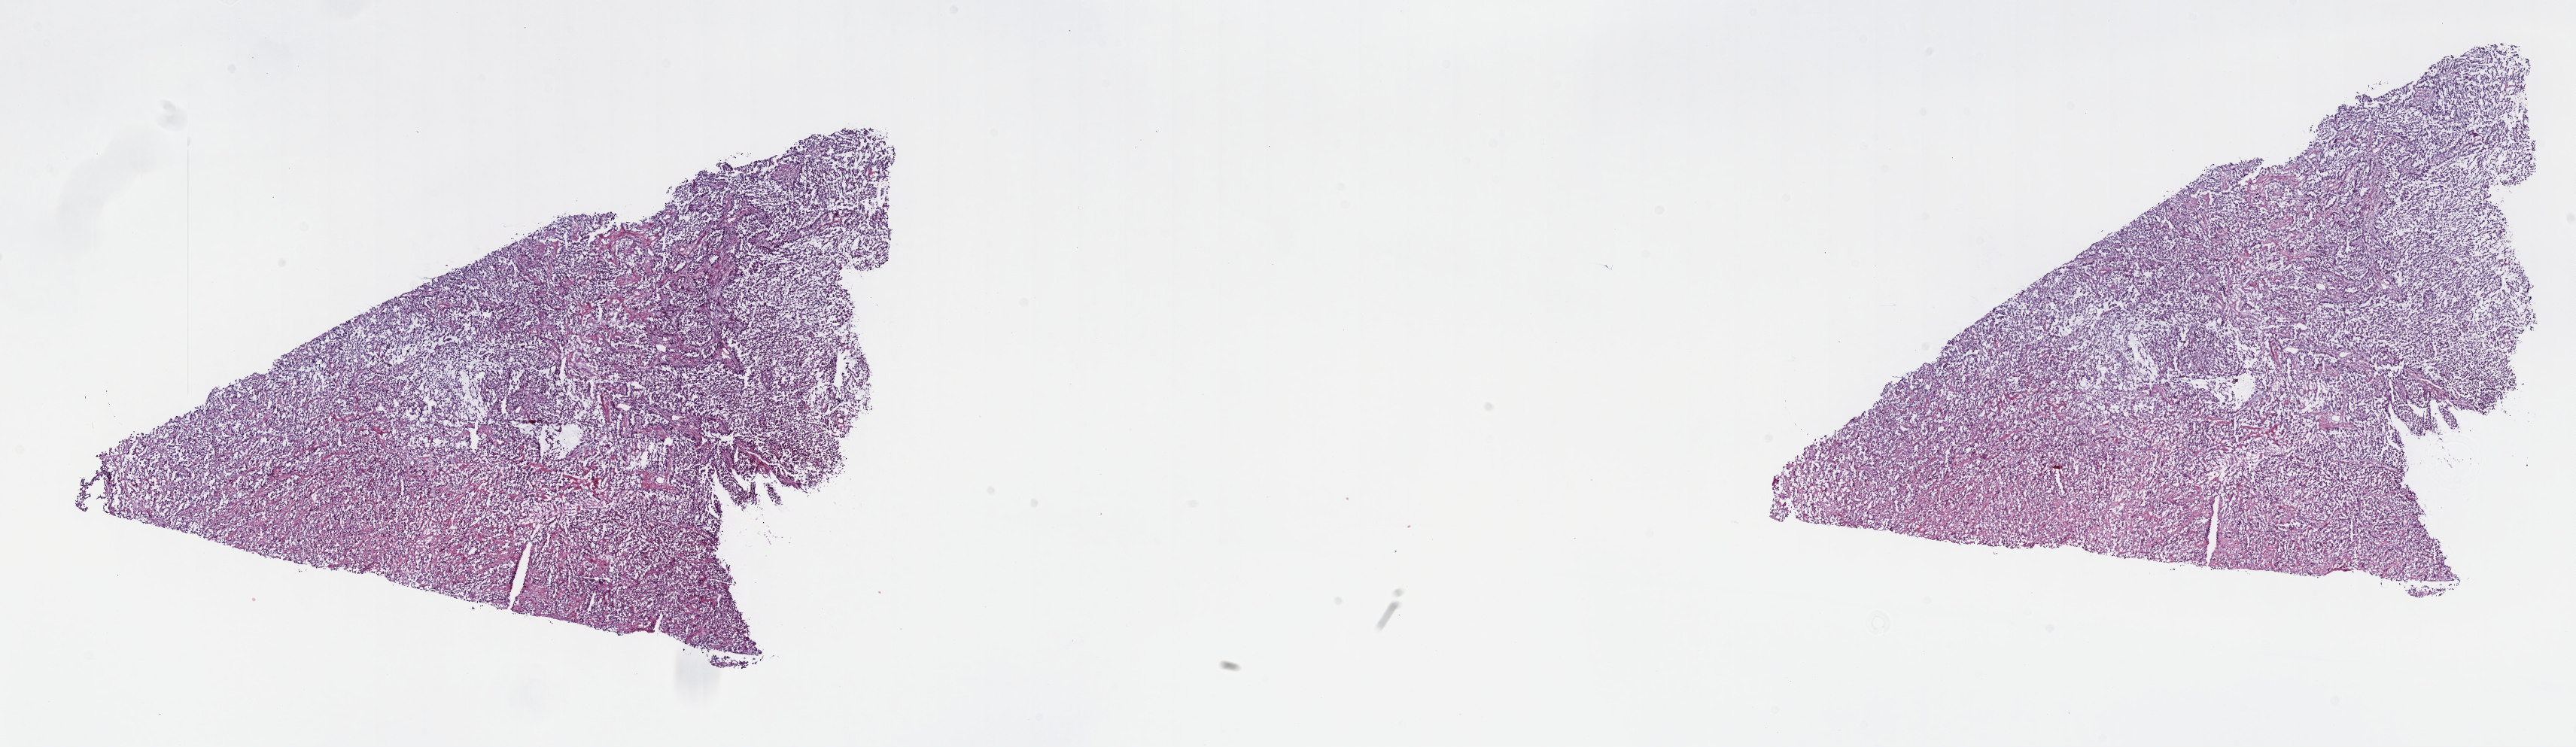
Hematoxylin and eosin (H&E) stained whole-slide image — low-resolution overview of the scanned area, about 27.7 x 8.0 mm (slide scanned at 40x), frozen section, primary tumour sample from the kidney. Female, age 69 years at initial diagnosis. Slide review estimates, as recorded: tumour cells 70%, tumour nuclei 75%, normal cells 0%, stromal cells 25%, necrosis 5%. Infiltration values recorded for this section: lymphocyte infiltration 0%, monocyte infiltration 10%, neutrophil infiltration 0%.
- pathologic diagnosis: Papillary adenocarcinoma, NOS
- AJCC pathologic stage: I
- TNM: T1a NX M0
- laterality: right